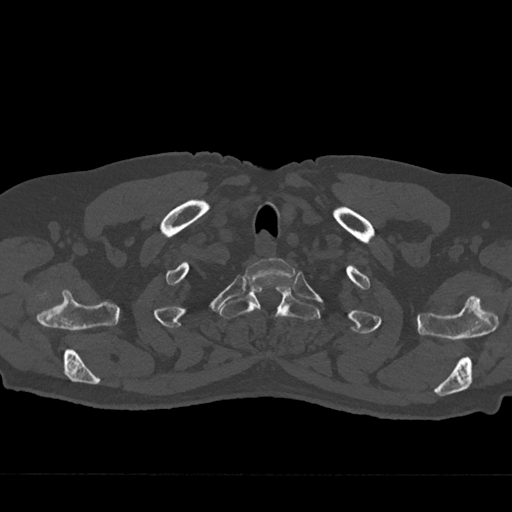
CT including the spine, one axial slice; bone window (W 1800 / L 400 HU); 512 × 512 image matrix, field of view 377 × 377 mm. Patient: male, 75 years. From the clinical record (not read from this slice): primary cancer: renal.
Structures marked on this image (semi-automatically segmented with operator editing):
- T1 vertebra: box from (x=244, y=258) to (x=294, y=283) px
- T2 vertebra: (x=220, y=287)–(x=319, y=320)